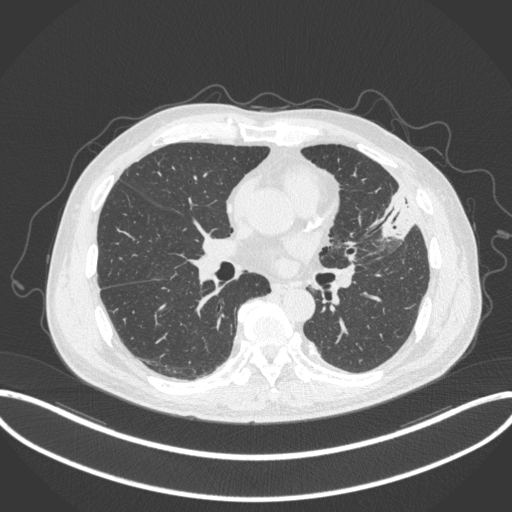
Chest CT, one axial slice; position 166 of 382 along the scan axis; reconstruction kernel B31f; 120 kVp; lung window (W 1500 / L -600 HU); 1 mm slice thickness; 512 × 512 image matrix. Patient: male, 64 years. From the clinical record (not read from this slice): clinical TNM (as recorded): T4 N1 M0; histopathological grade: G3.
Outlined on this slice (rectangle marked by the reading radiologist):
- lung tumour (recorded histology: adenocarcinoma): bounding box (x1, y1, x2, y2) in pixels: (368, 182, 420, 248)